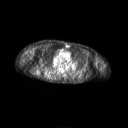
FDG PET of an extremity soft-tissue mass (from a PET/CT study), one axial slice. Slice 174 of 267 in the series (ordered by position). 3.27 mm slice thickness. 128 × 128 image matrix, field of view 700 × 700 mm. Patient: male, 61 years. Case-level facts recorded for this patient, not image findings: histological type: pleiomorphic spindle cell undifferentiated; grade: high; site of the primary tumour: right parascapusular.
Annotated regions visible in this slice (expert contour drawn on MRI and transferred to this co-registered scan by the dataset authors):
- gross tumour volume including surrounding oedema: bounding box <47,74,55,77> (left, top, right, bottom; pixels)